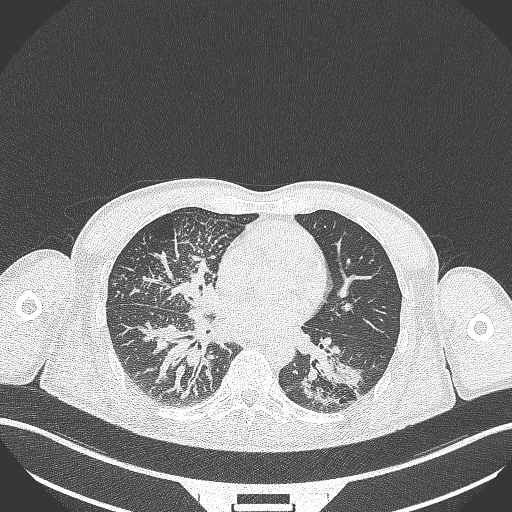
Chest CT, one axial slice; slice 145 of 348 in the series (ordered by position); reconstruction kernel B70f; 120 kVp; lung window (W 1500 / L -600 HU); 512 × 512 image matrix, field of view 400 × 400 mm. Male patient, age 49 years. From the clinical record (not read from this slice): clinical TNM (as recorded): T2b N1 M0.
Structures marked on this image (bounding box drawn by a radiologist):
- lung tumour (recorded histology: adenocarcinoma): bounding box (x1, y1, x2, y2) in pixels: (298, 348, 369, 405)